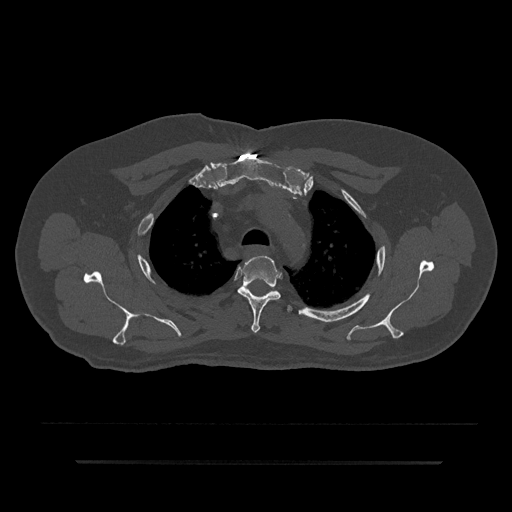
CT including the spine, one axial slice. Slice 653 of 797 in the series (ordered by position). Reconstruction kernel Br40s/3. Bone window (W 1800 / L 400 HU). 0.5 mm slice thickness. 512 × 512 image matrix, field of view 464 × 464 mm. Male patient, age 59 years. Case-level facts recorded for this patient, not image findings: primary cancer: bile ducts.
Structures marked on this image (semi-automatic segmentation, software-assisted and operator-edited):
- T3 vertebra: bounding box (x1, y1, x2, y2) in pixels: (237, 255, 281, 333)
- T4 vertebra: (287, 305, 293, 311)